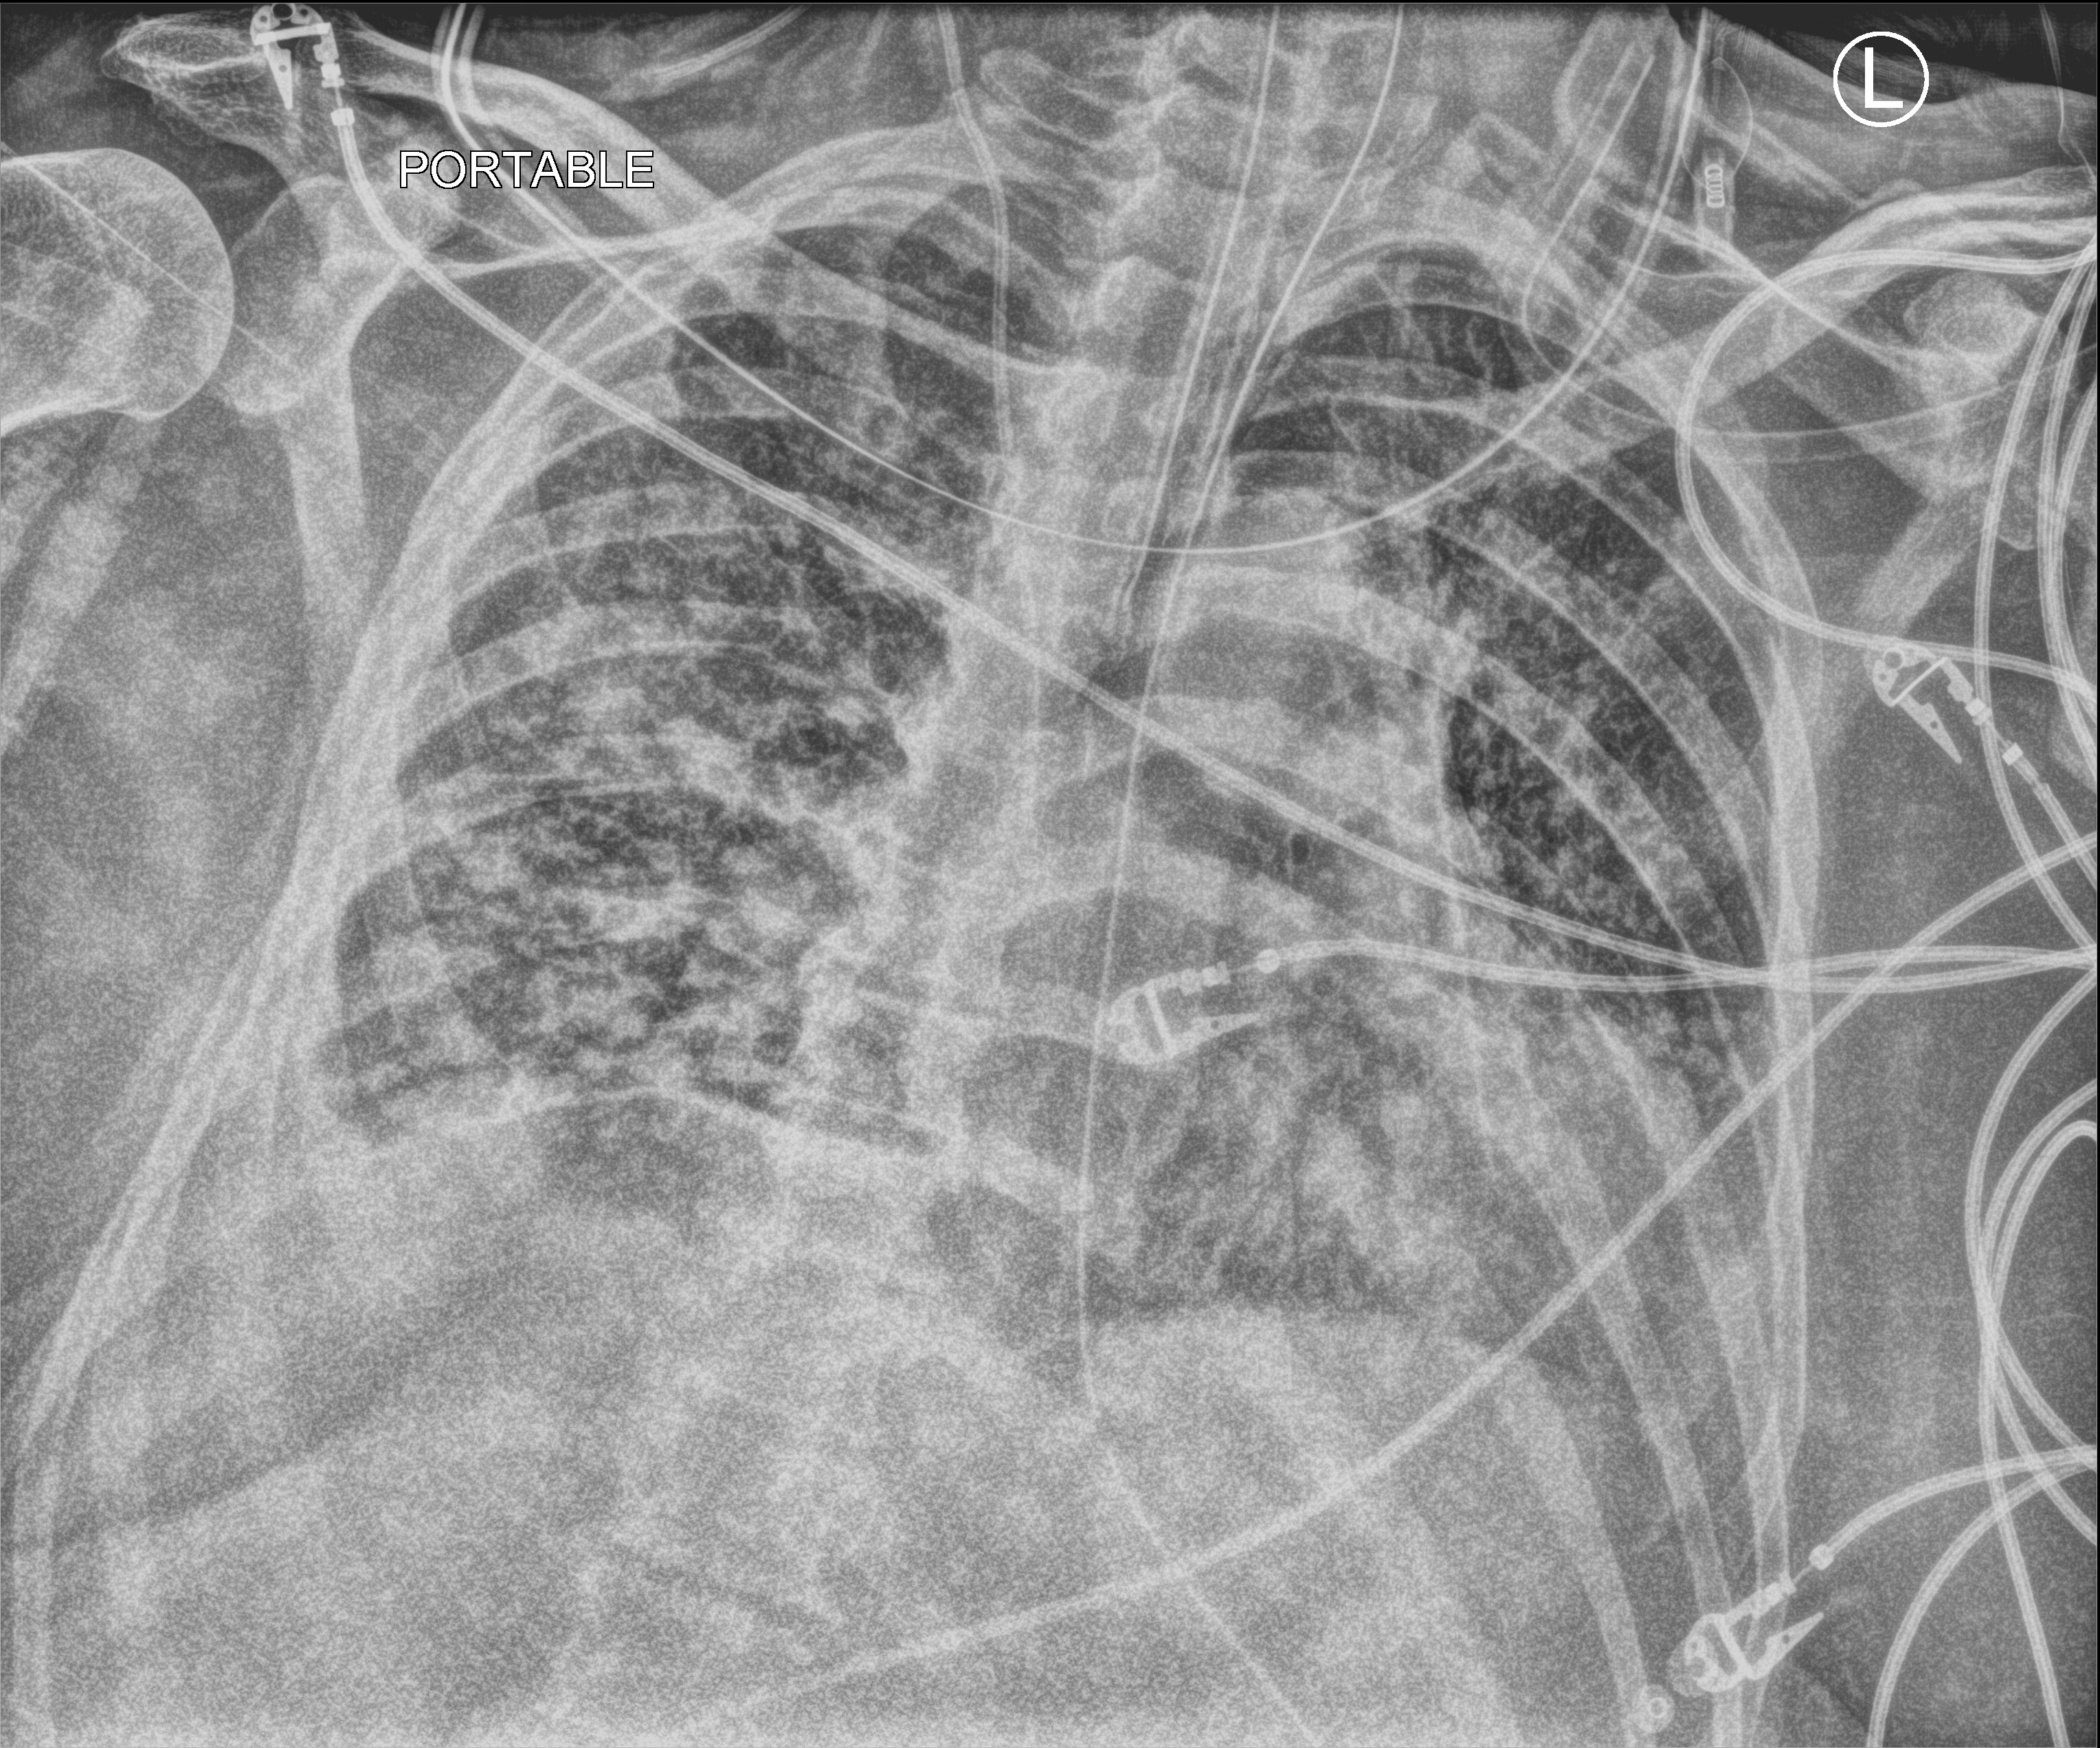
Chest X-ray (portable), anteroposterior (AP) projection. Patient hospitalised with COVID-19; male, aged 60–74 years.
Hospital-stay facts (about this admission, not read from this image; timing relative to this image not recorded):
- admitted to intensive care during this hospital stay: yes
- length of hospital stay: 40 days